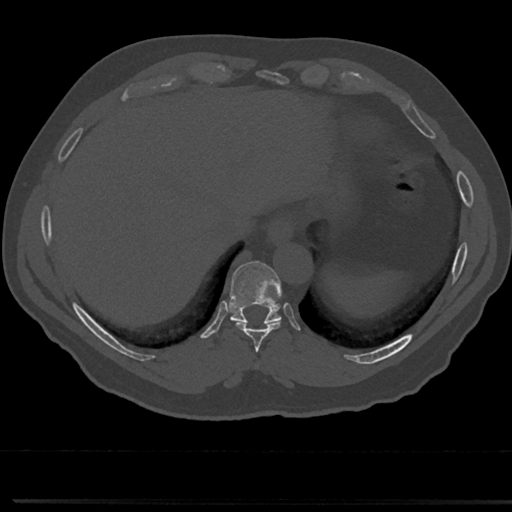
CT including the spine, one axial slice; slice 283 of 817 in the series (ordered by position); reconstruction kernel Br40s/3; bone window (W 1800 / L 400 HU); 512 × 512 image matrix. Patient: male, 61 years. From the clinical record (not read from this slice): primary cancer: prostate.
Outlined on this slice (semi-automatic segmentation, software-assisted and operator-edited):
- T8 vertebra: bounding box [x1, y1, x2, y2] px = [254, 354, 264, 372]
- T9 vertebra: [212, 262, 303, 350]